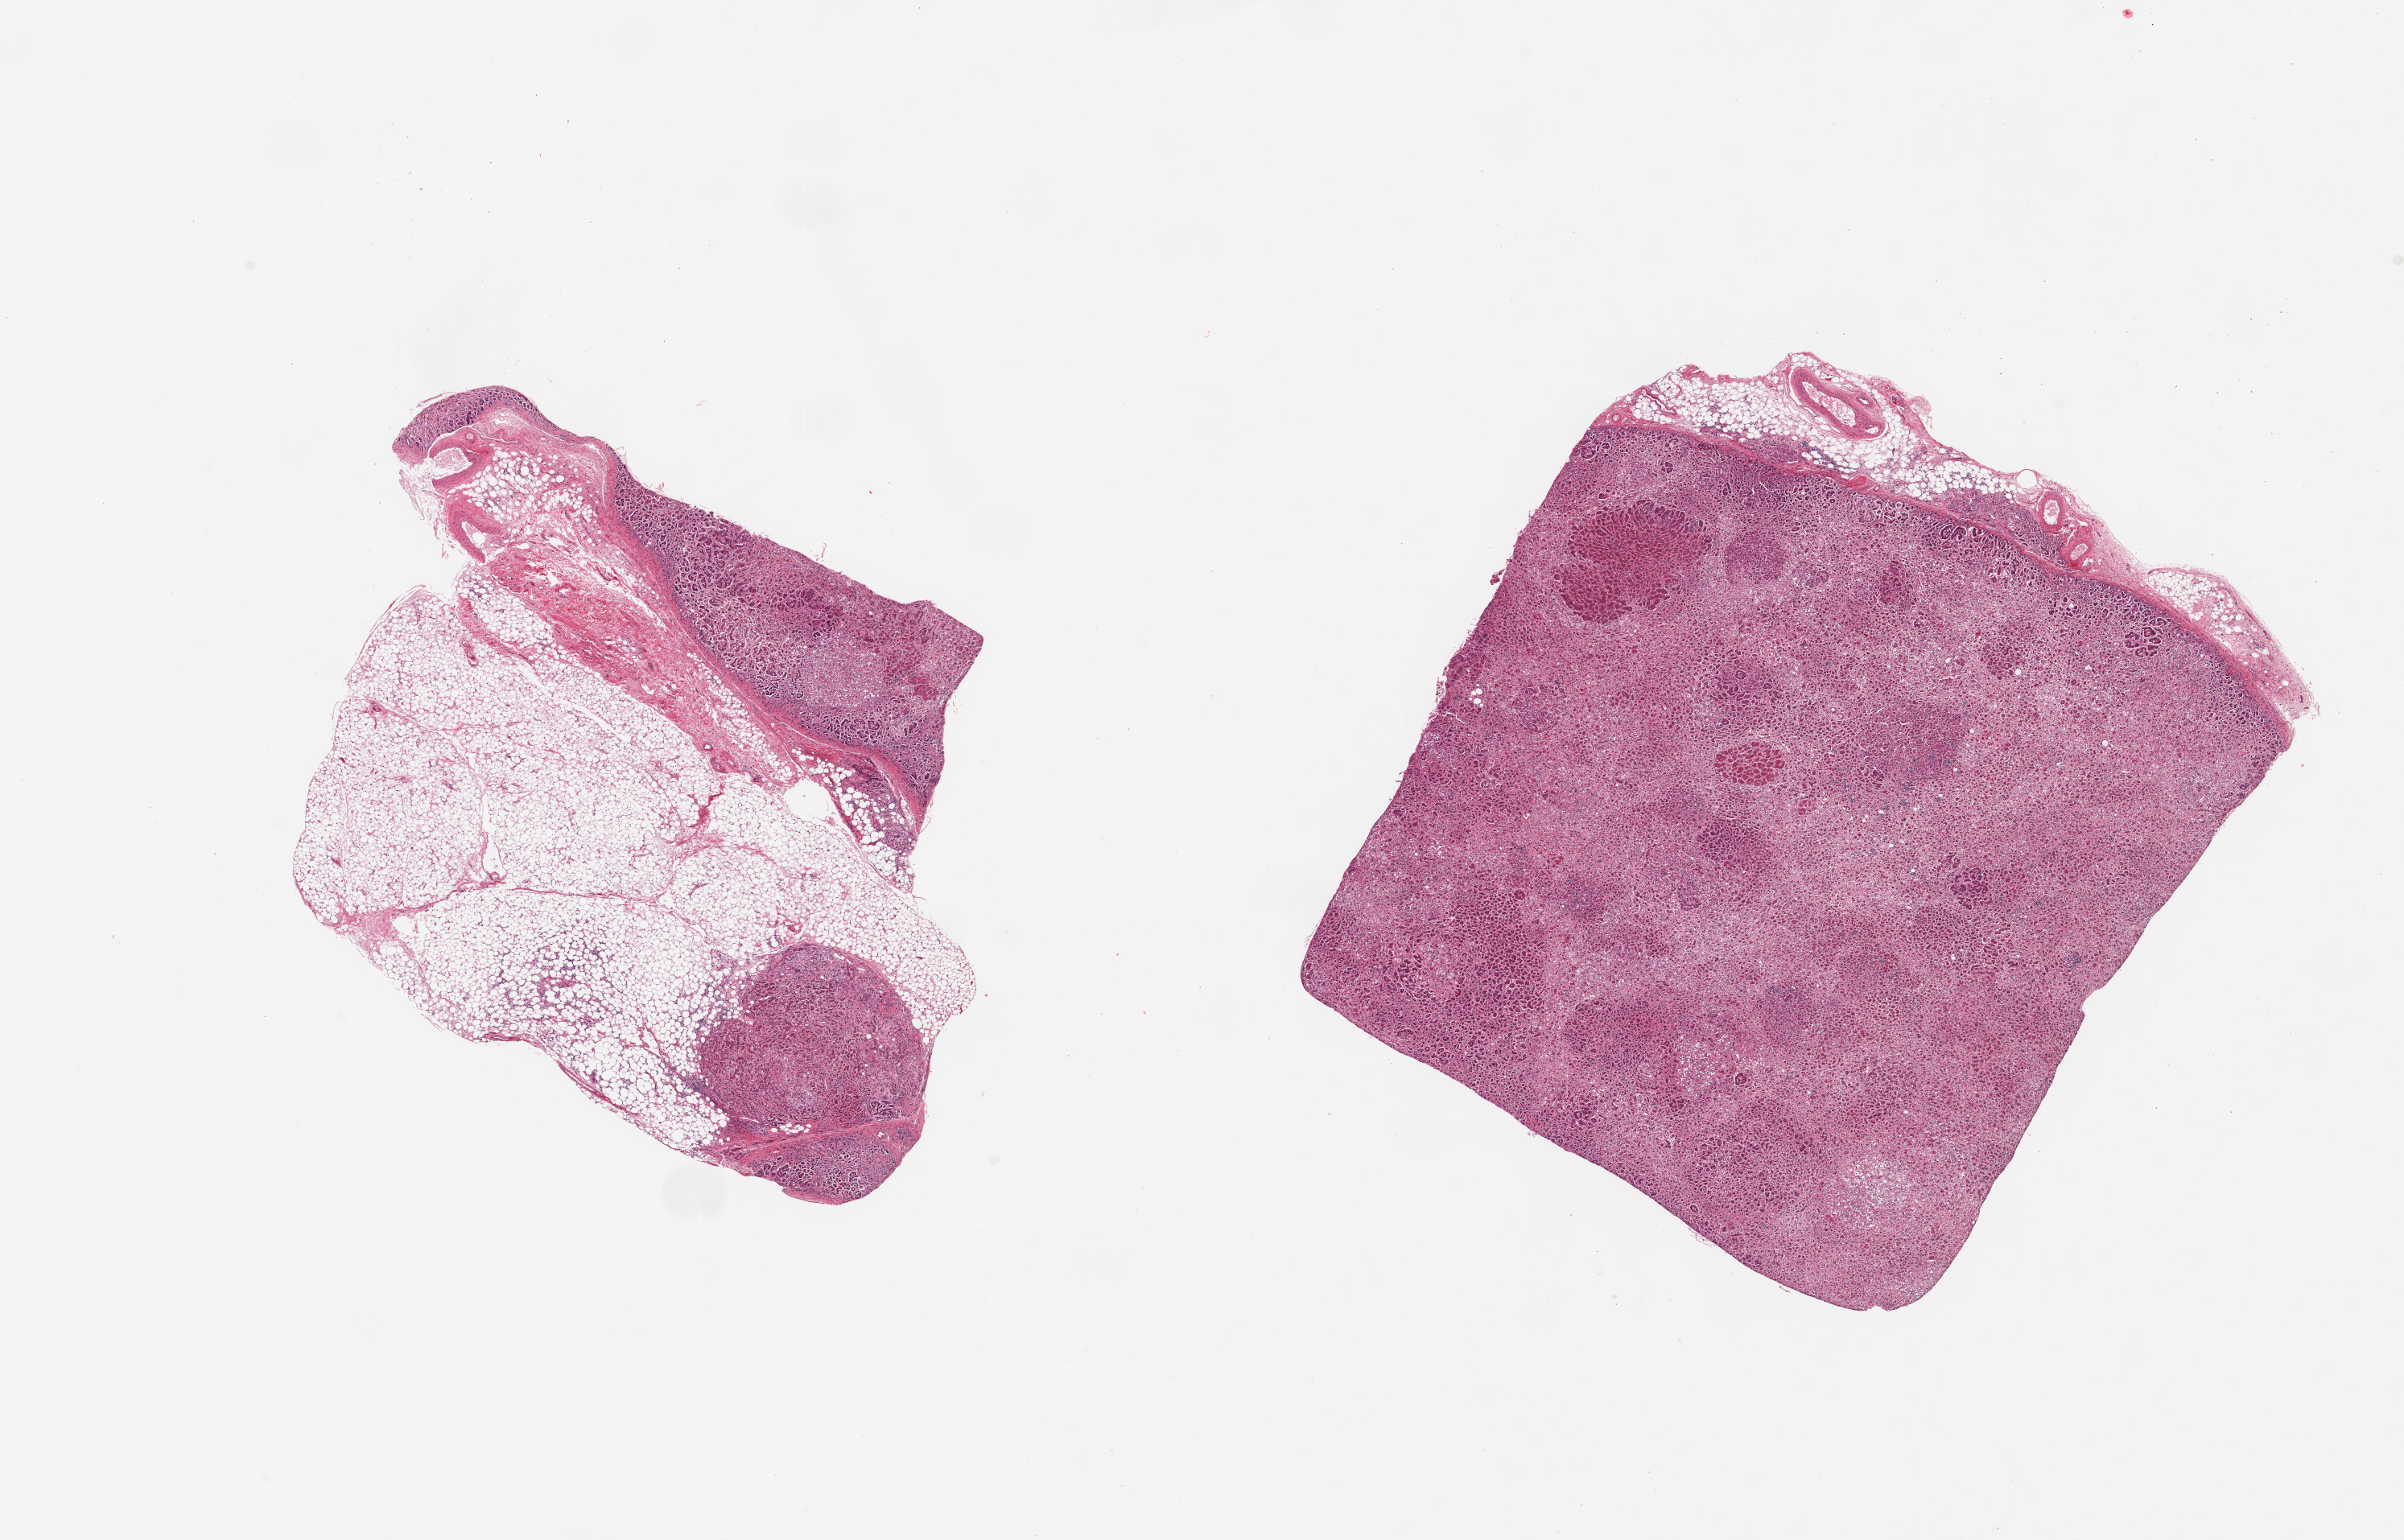
Whole-slide image, haematoxylin and eosin stain — whole scanned area (about 23.6 x 15.1 mm, from a 20x scan) shown as a low-resolution overview; PAXgene-fixed paraffin-embedded (PFPE) section; target tissue: adrenal gland; tissue donor sample.
Review note (as recorded): 2 pieces; 70% and 10% external fat; focal severe autolysis of adrenal cortex.